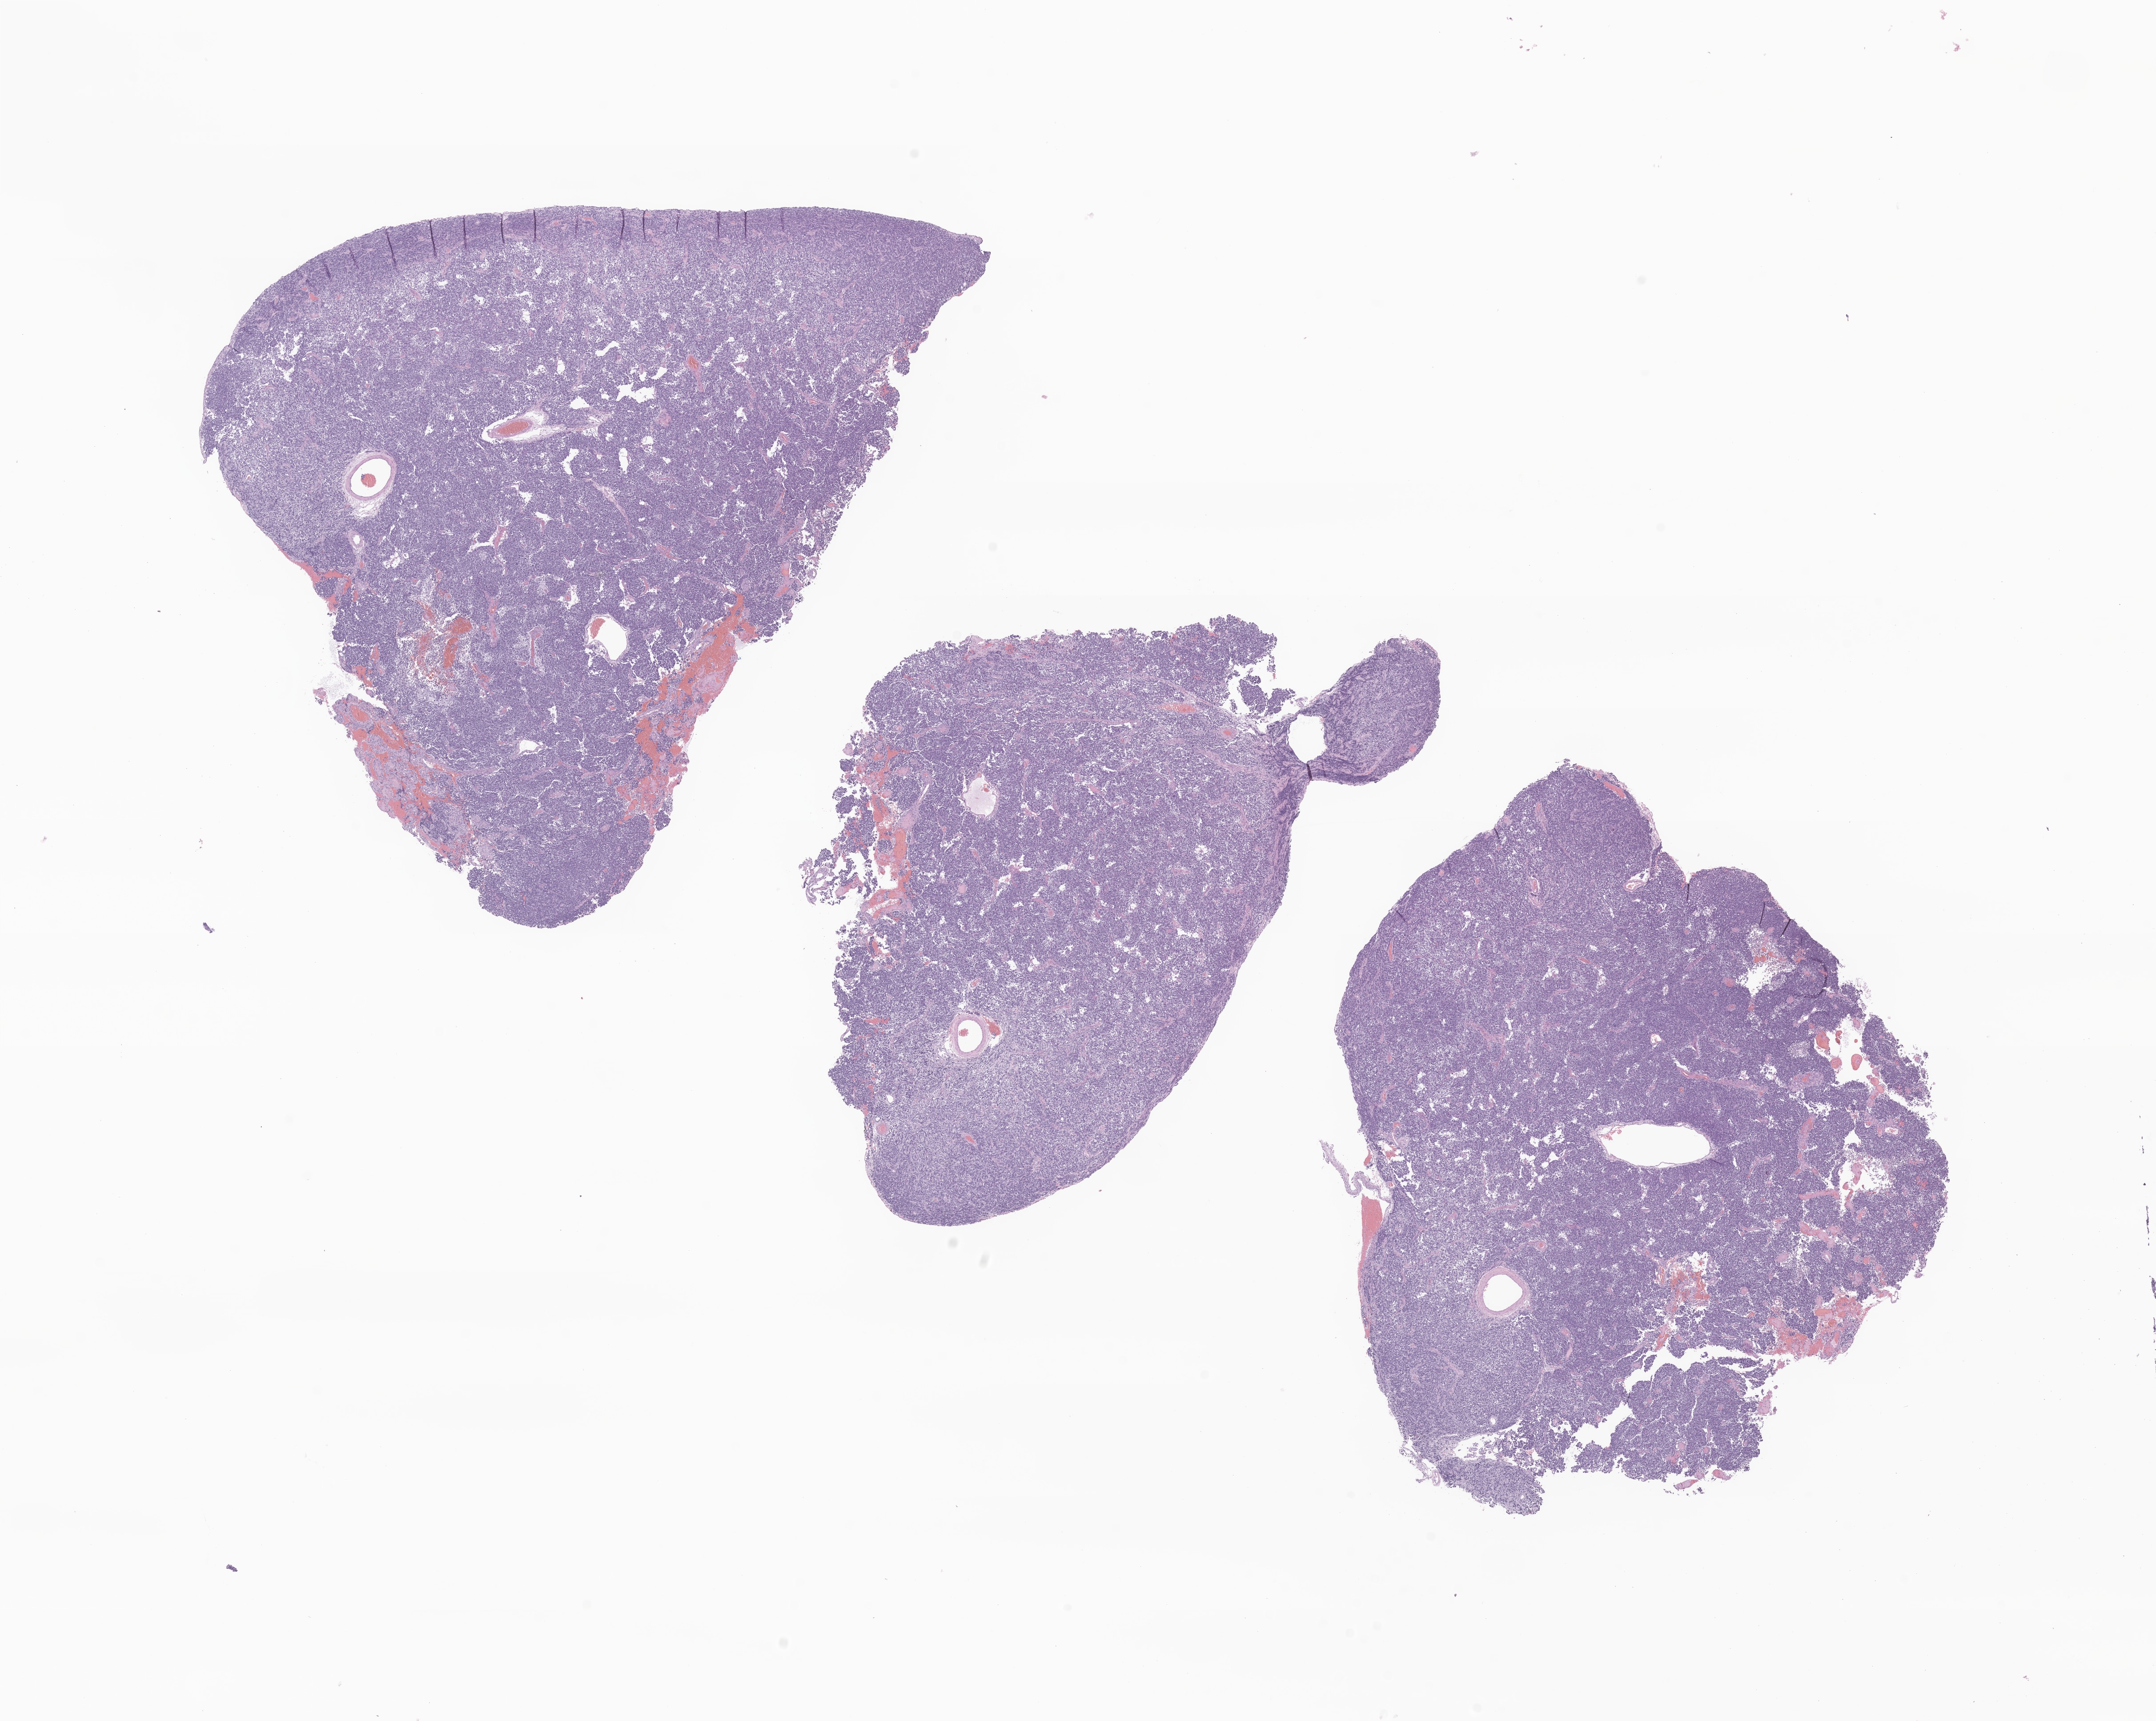
Haematoxylin and eosin whole-slide image of tumor tissue from the cerebellum, a low-resolution overview of the entire scanned area, about 20.4 x 16.3 mm. FFPE section. Patient: male, age 60 months.
Recorded diagnosis: Large cell medulloblastoma.